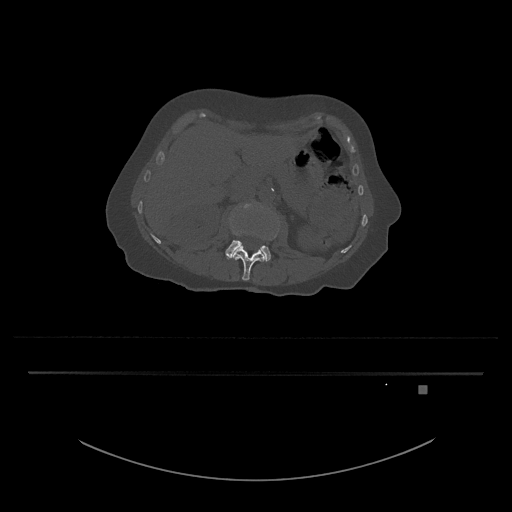
CT including the spine, one axial slice. Position 464 of 797 along the scan axis. Reconstruction kernel Br40s/3. Bone window (W 1800 / L 400 HU). 0.5 mm slice thickness. 512 × 512 image matrix, field of view 500 × 500 mm. Female patient, age 57 years. Case-level facts recorded for this patient, not image findings: primary cancer: cervical.
Structures marked on this image (semi-automatically segmented with operator editing):
- L3 vertebra: bounding box (x1, y1, x2, y2) in pixels: (225, 203, 279, 262)